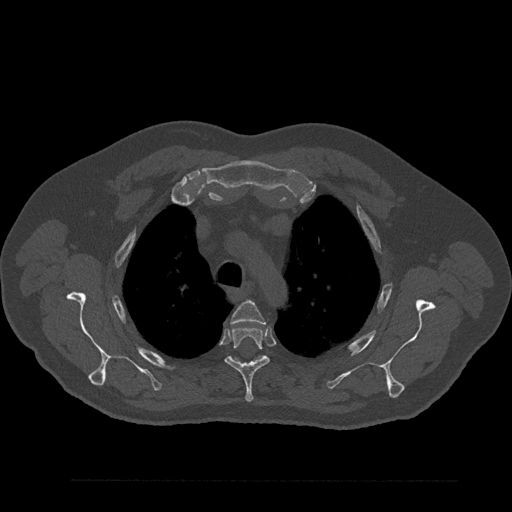
CT including the spine, one axial slice. Slice 647 of 797 in the series (ordered by position). Reconstruction kernel Br40s/3. 120 kVp. Bone window (W 1800 / L 400 HU). 512 × 512 image matrix, field of view 430 × 430 mm. Patient: male, 61 years. Case-level facts recorded for this patient, not image findings: primary cancer: prostate.
Outlined on this slice (semi-automatic segmentation, software-assisted and operator-edited):
- T3 vertebra: bounding box (x1, y1, x2, y2) in pixels: (231, 301, 265, 324)
- T4 vertebra: (225, 326, 270, 402)
- T5 vertebra: (234, 356, 265, 362)